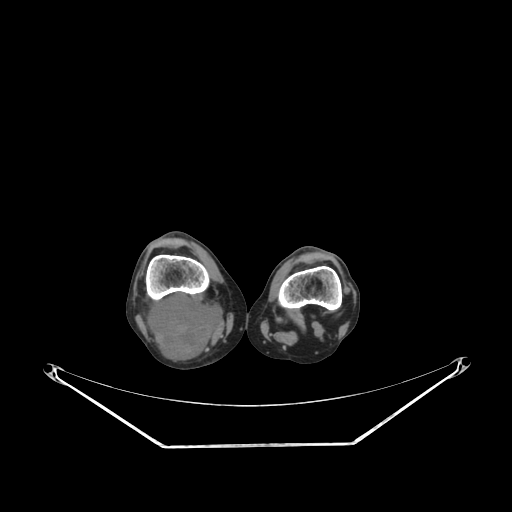
CT of an extremity soft-tissue mass (from a PET/CT study), one axial slice. Slice 174 of 267 in the series (ordered by position). Reconstruction kernel SOFT. Soft-tissue window (W 400 / L 40 HU). 3.75 mm slice thickness. 512 × 512 image matrix. Female patient. From the clinical record (not read from this slice): histological type: liposarcoma; site of the primary tumour: right thigh.
Structures marked on this image (expert contour drawn on MRI and transferred to this co-registered scan by the dataset authors):
- gross tumour volume (mass): bounding box <144,291,225,359> (left, top, right, bottom; pixels)